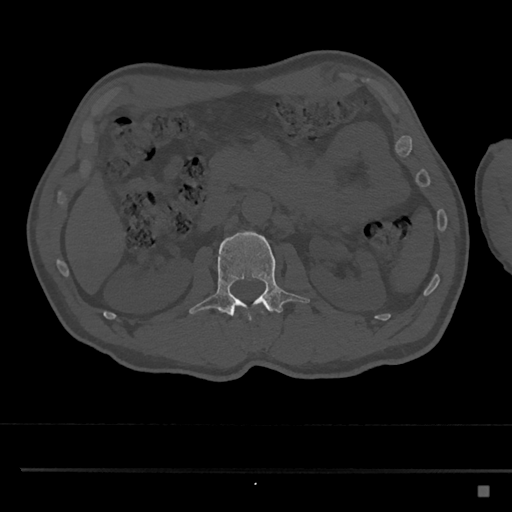
CT including the spine, one axial slice. Position 769 of 797 along the scan axis. Reconstruction kernel Br40s/3. Bone window (W 1800 / L 400 HU). 512 × 512 image matrix, field of view 391 × 391 mm. Patient: male, 59 years. From the clinical record (not read from this slice): primary cancer: prostate.
Structures marked on this image (semi-automatic segmentation, software-assisted and operator-edited):
- L2 vertebra: bounding box <189,230,310,345> (left, top, right, bottom; pixels)